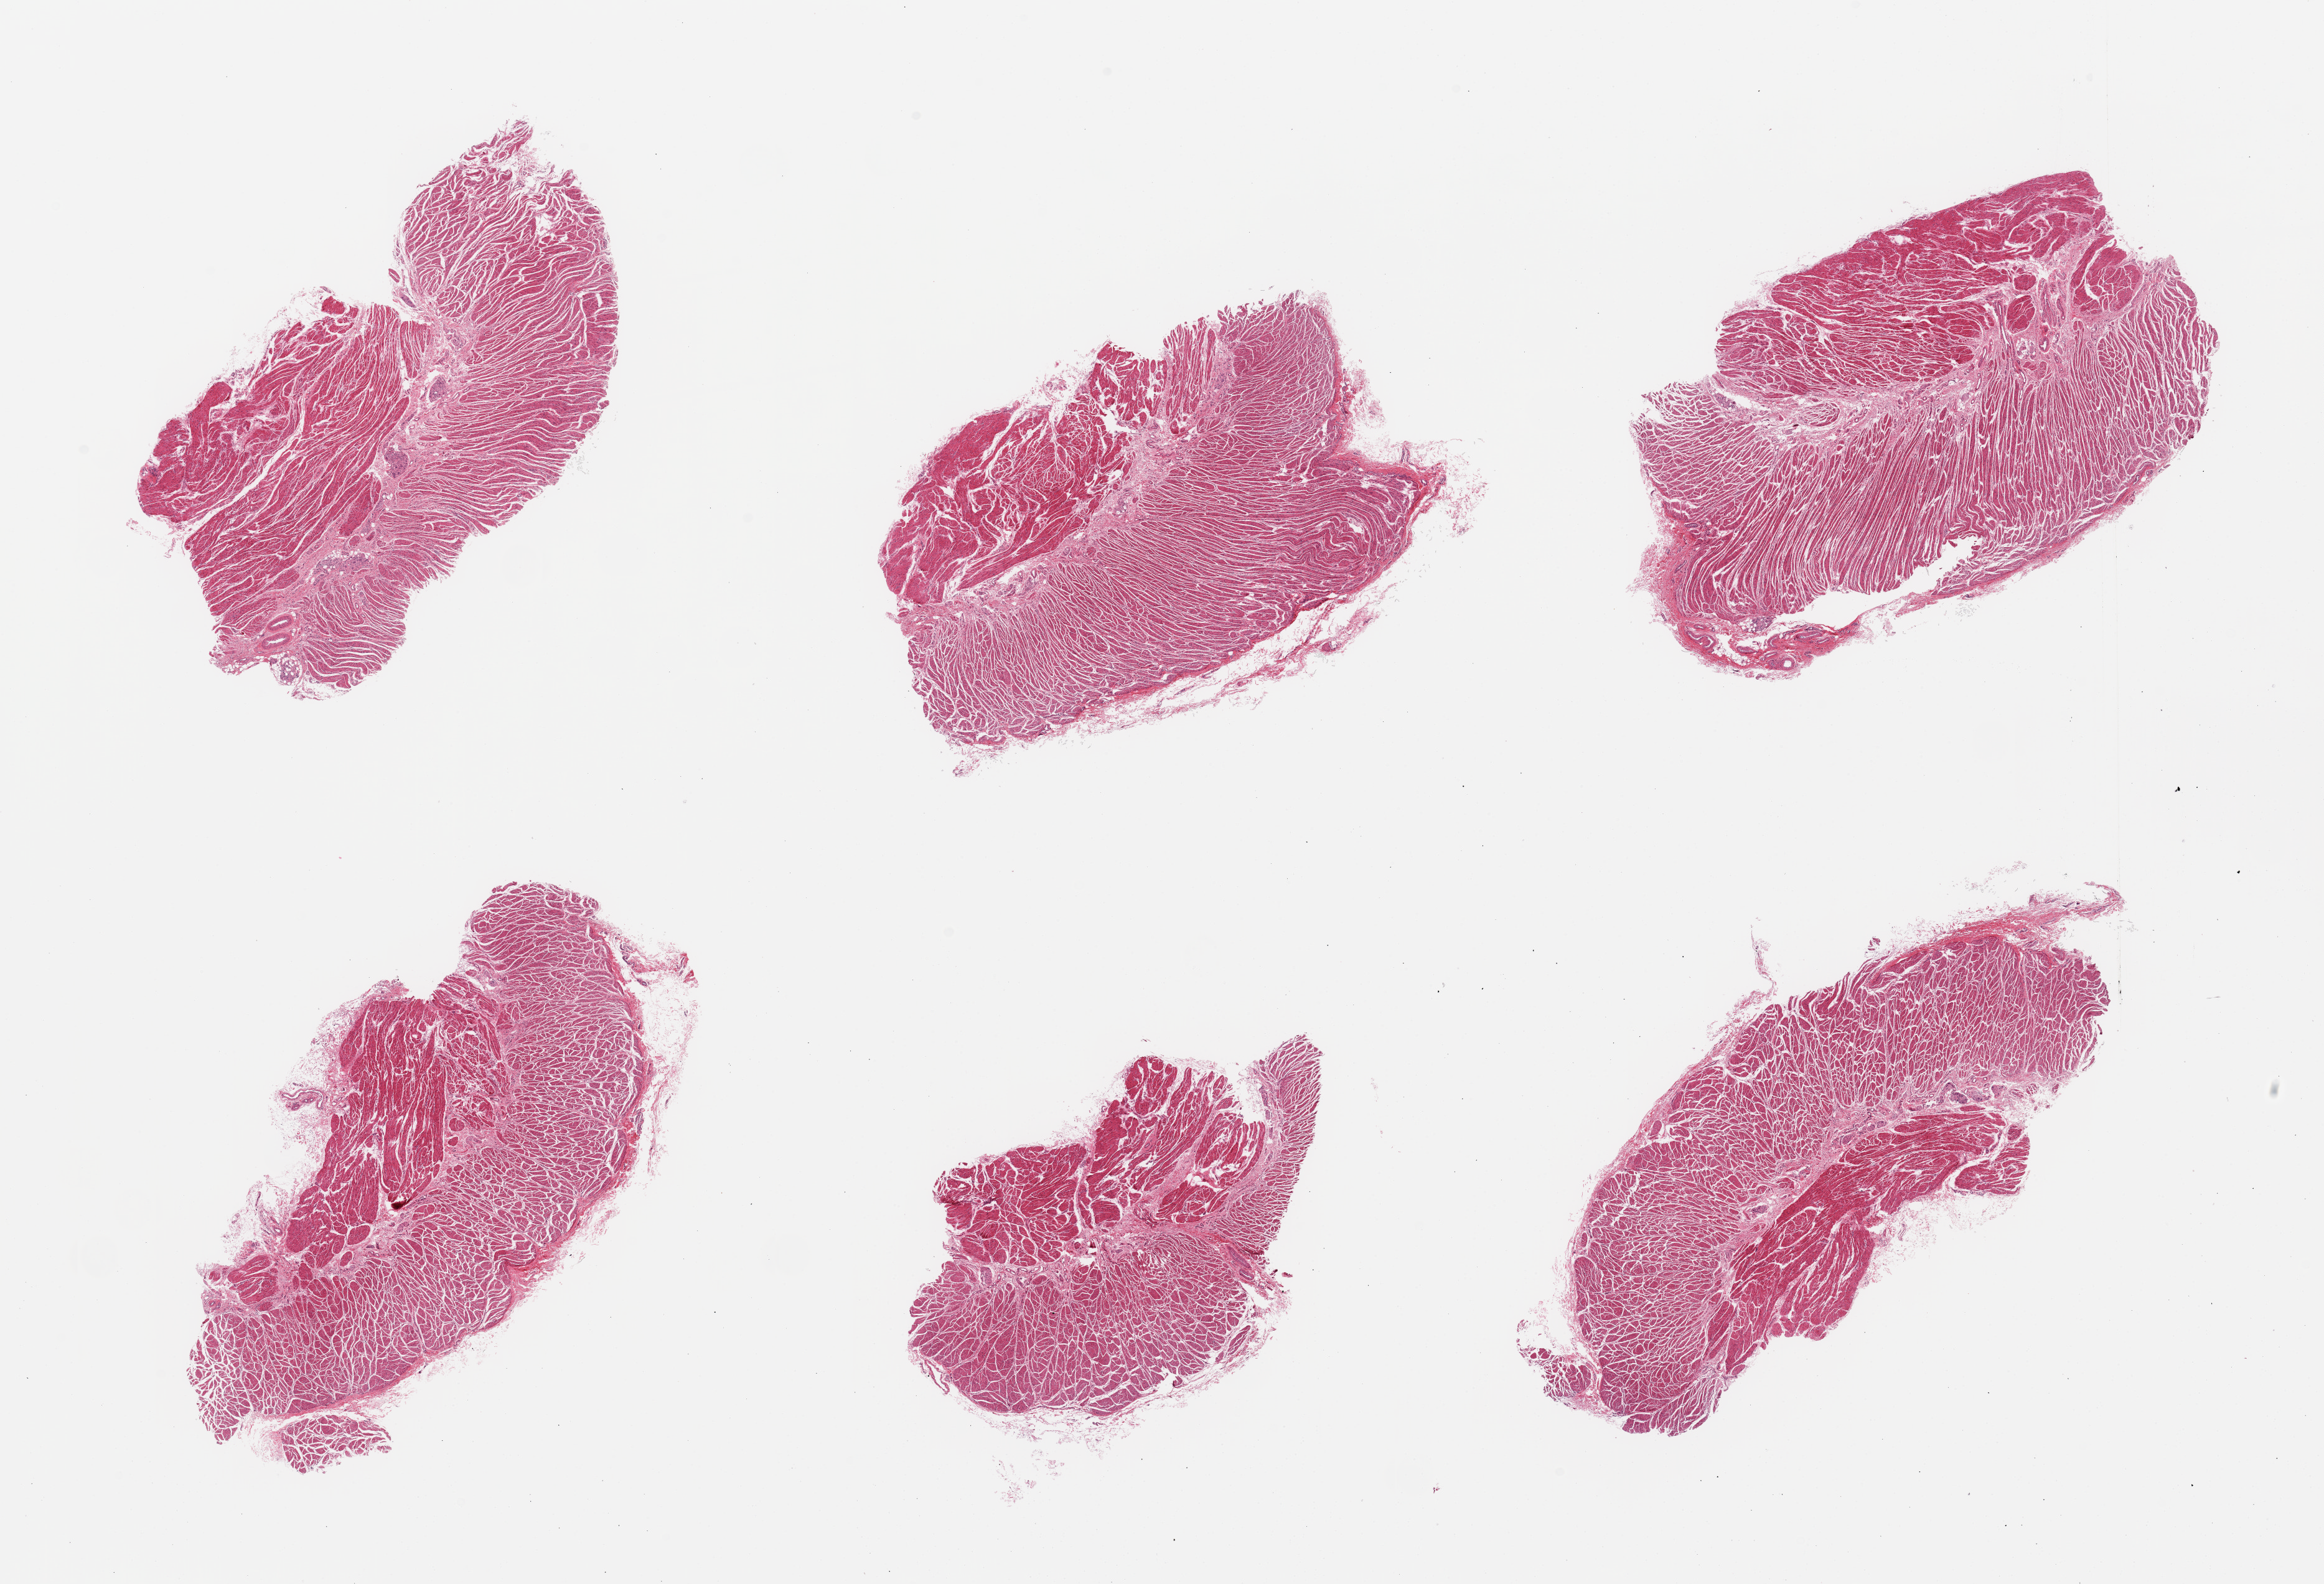
Hematoxylin and eosin (H&E) whole-slide image — shown as a low-resolution overview of the whole scanned area (about 29.5 x 20.1 mm, acquisition: 20x scan). PAXgene-fixed, paraffin-embedded tissue. Section of gastroesophageal junction (target tissue). Donor tissue sample. Donor sex: female.
* review note (as recorded): 6 pieces, all muscularis, good specimens